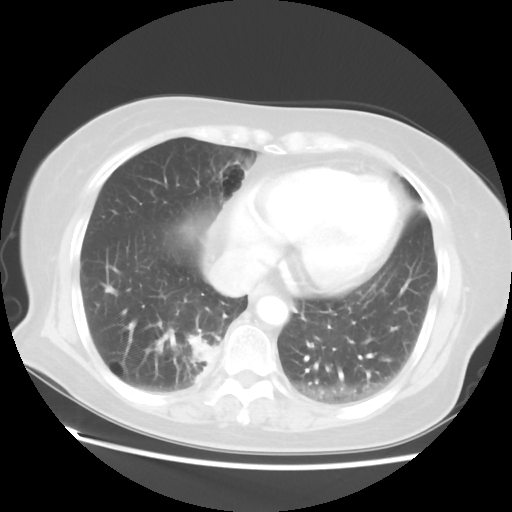
Chest CT, one axial slice; slice 17 of 52 in the series (ordered by position); 120 kVp; lung window (W 1500 / L -600 HU); 512 × 512 image matrix, field of view 356 × 356 mm. Patient: female, 69 years. Case-level facts recorded for this patient, not image findings: clinical TNM (as recorded): T2 N1 M1a.
Outlined on this slice (bounding box drawn by a radiologist):
- lung tumour (recorded histology: adenocarcinoma): bounding box (x1, y1, x2, y2) in pixels: (184, 333, 217, 388)